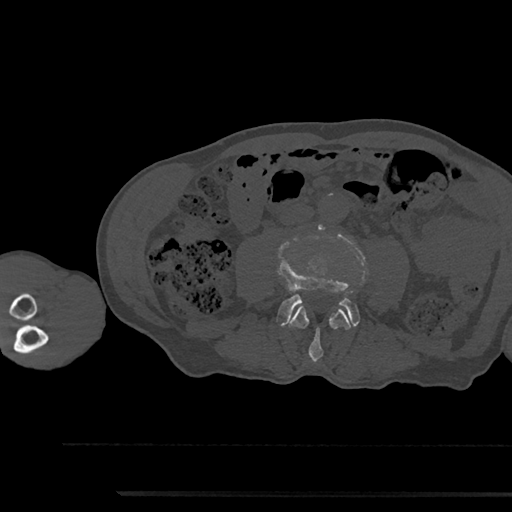
CT including the spine, one axial slice. Slice 446 of 797 in the series (ordered by position). Bone window (W 1800 / L 400 HU). 512 × 512 image matrix, field of view 367 × 367 mm. Male patient, age 79 years. From the clinical record (not read from this slice): primary cancer: prostate.
Annotated regions visible in this slice (semi-automatically segmented with operator editing):
- L3 vertebra: bounding box (x1, y1, x2, y2) in pixels: (289, 304, 351, 362)
- L4 vertebra: (278, 257, 359, 326)